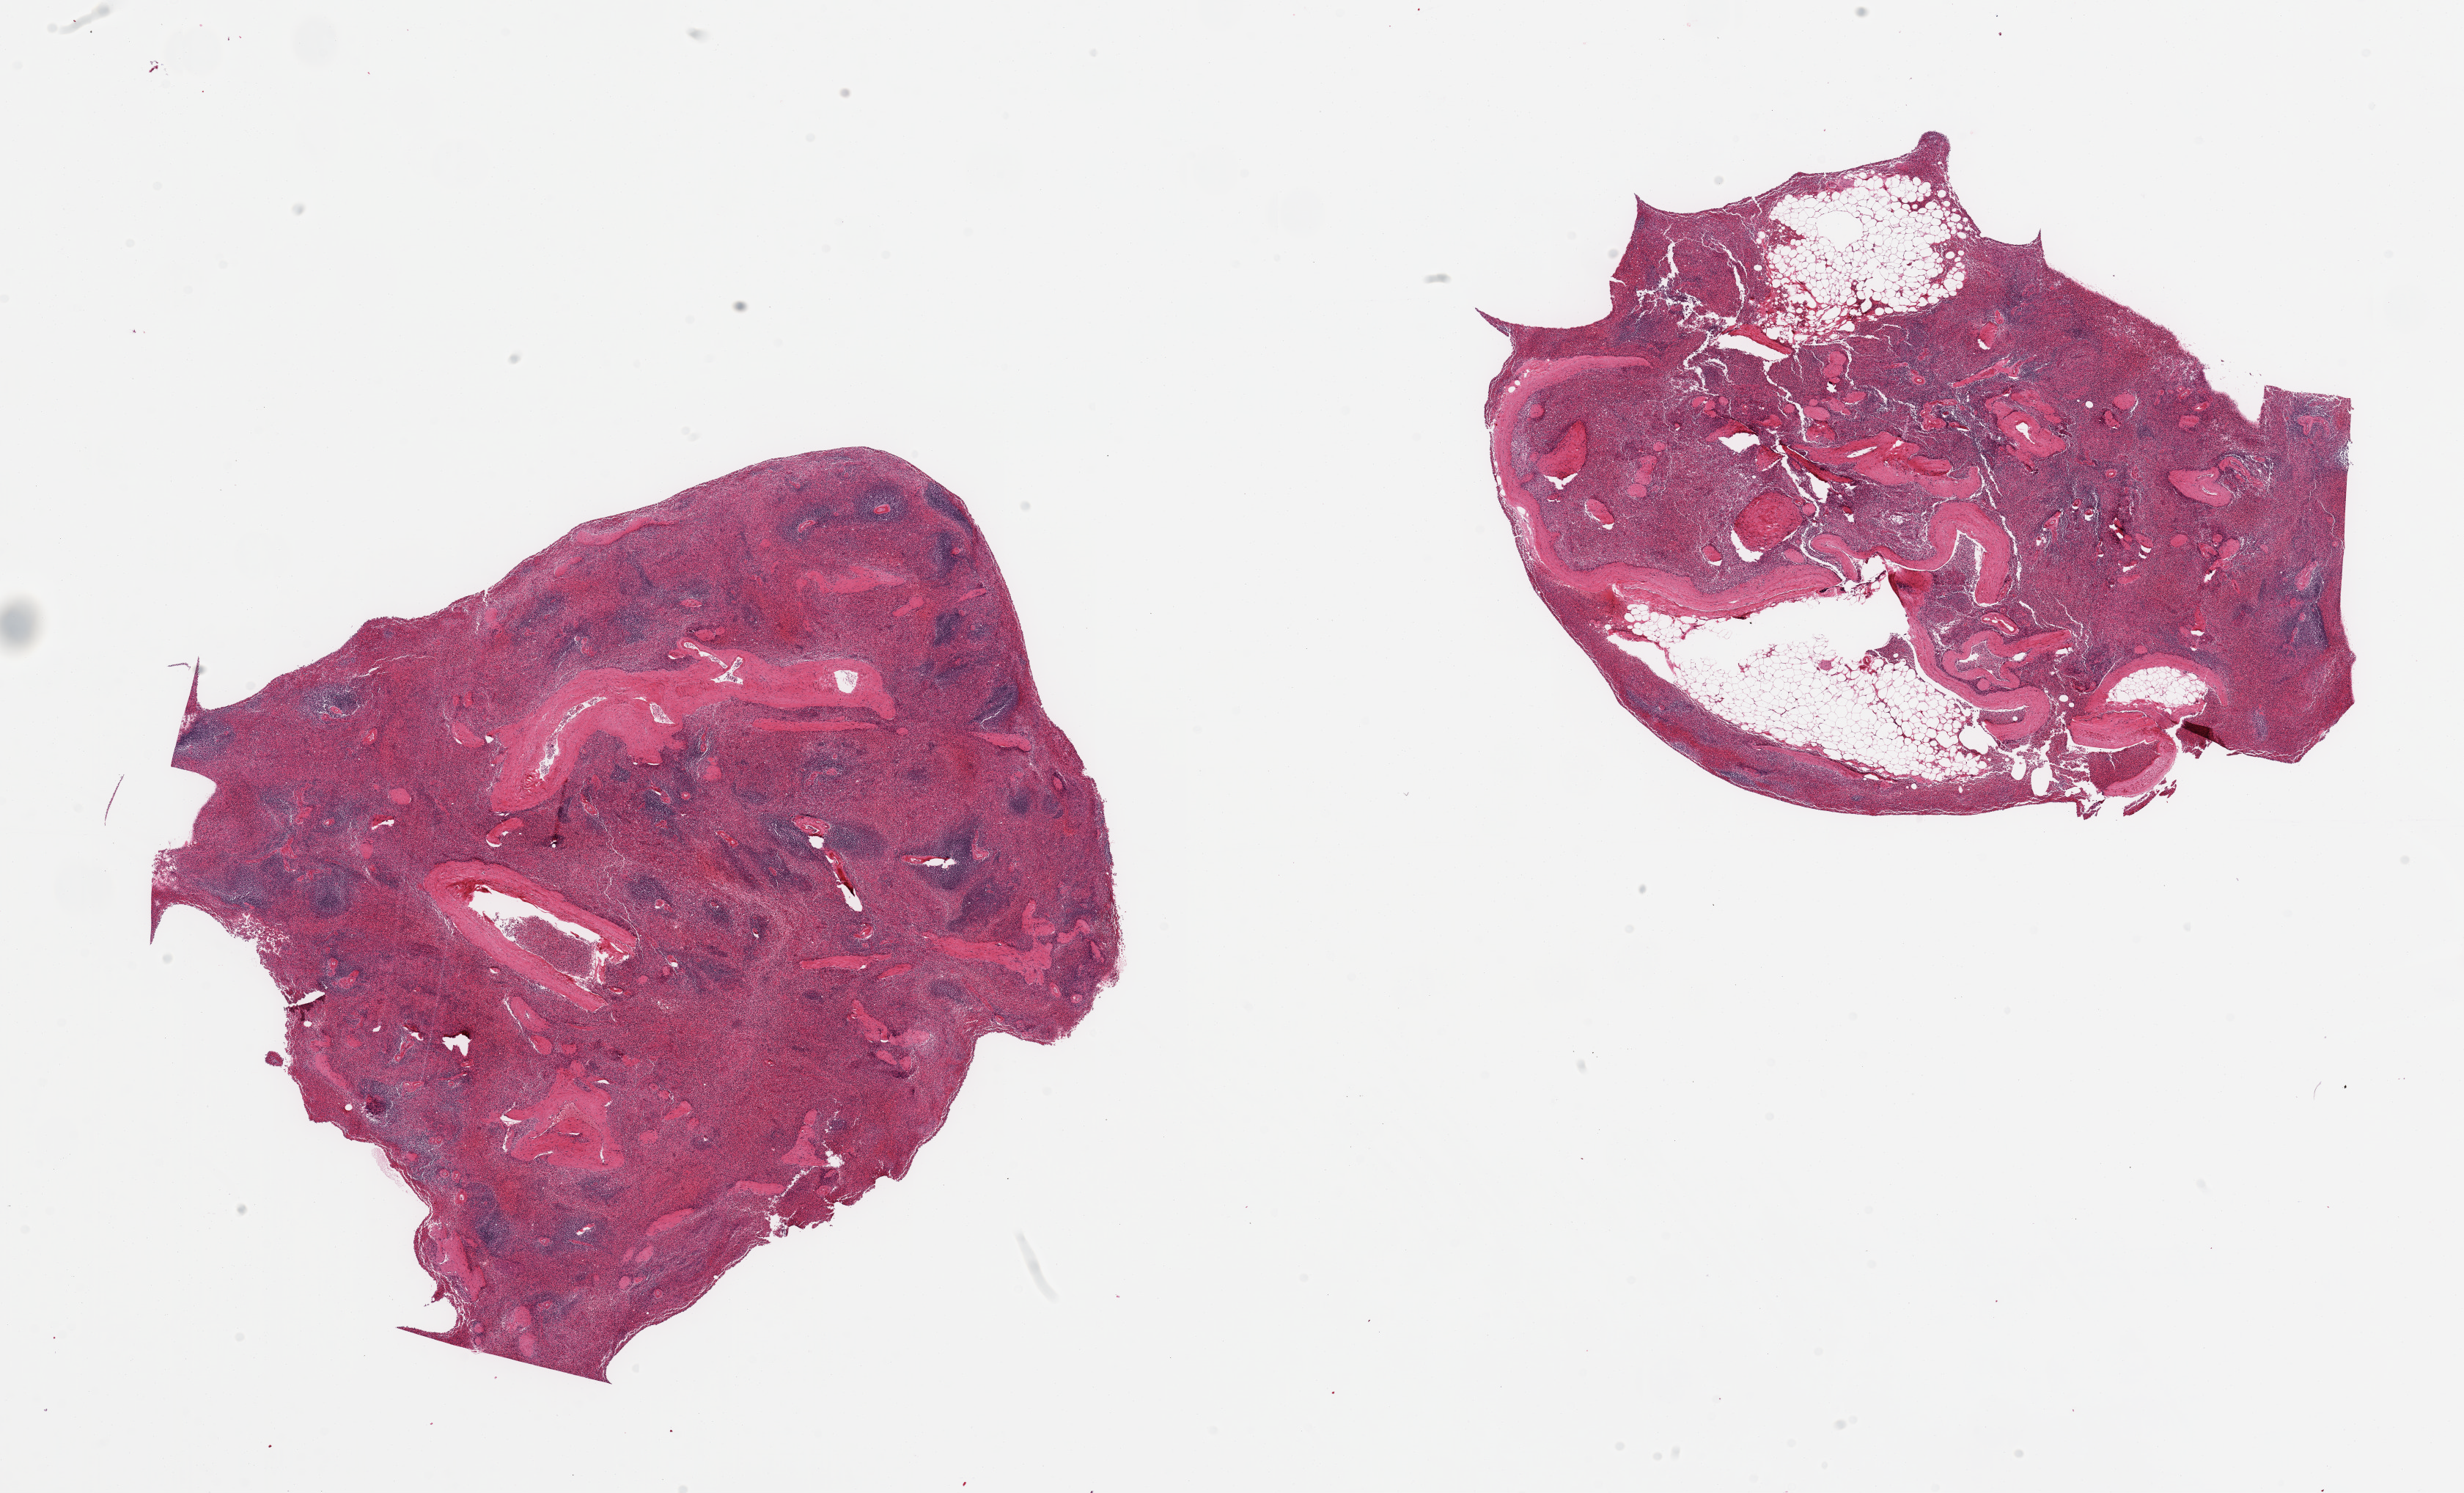
Hematoxylin and eosin (H&E) whole-slide image — a low-resolution overview of the entire scanned area, about 26.6 x 16.1 mm (acquisition: 20x scan), PAXgene-fixed, paraffin-embedded tissue, section of spleen (target tissue), donor tissue sample.
• reviewer comment on this tissue sample: 2 pieces; one piece include 20% fat